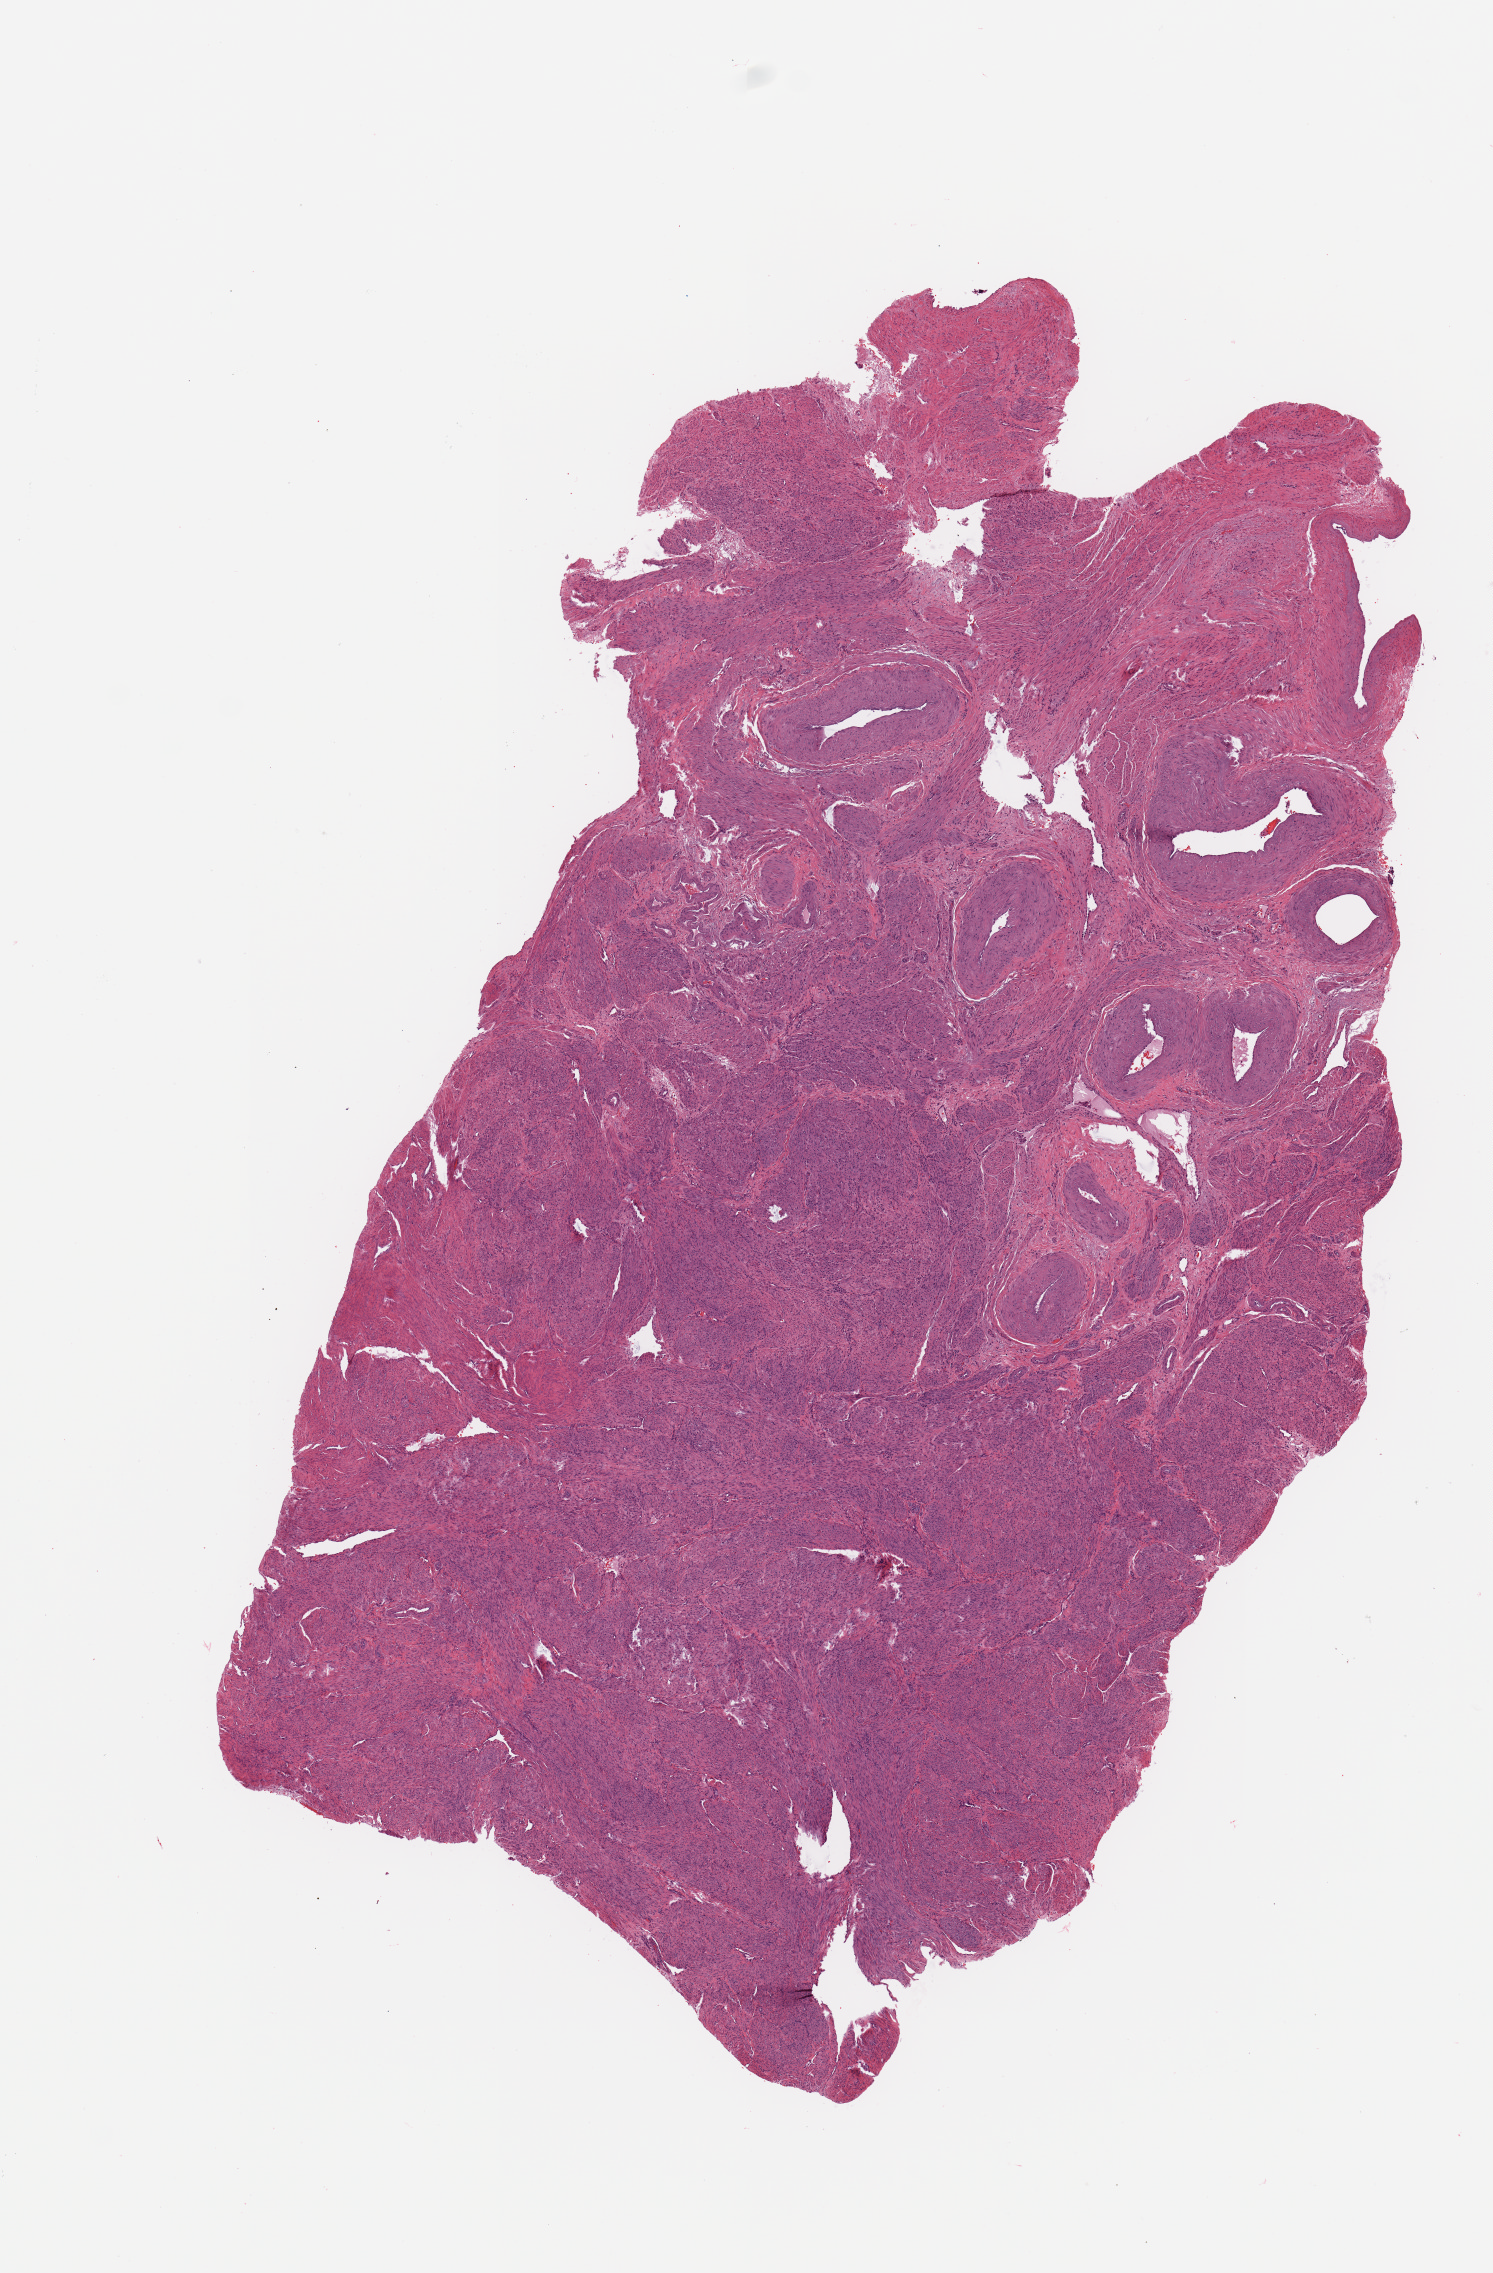
Whole-slide histology image, H&E, a low-resolution overview of the entire scanned area, about 5.9 x 9.0 mm (from a 20x scan), uterus, normal (non-tumour) tissue. Female, 55 y/o.
- this section: normal (non-tumour) tissue from the same patient
- patient diagnosis: Endometrioid adenocarcinoma, NOS